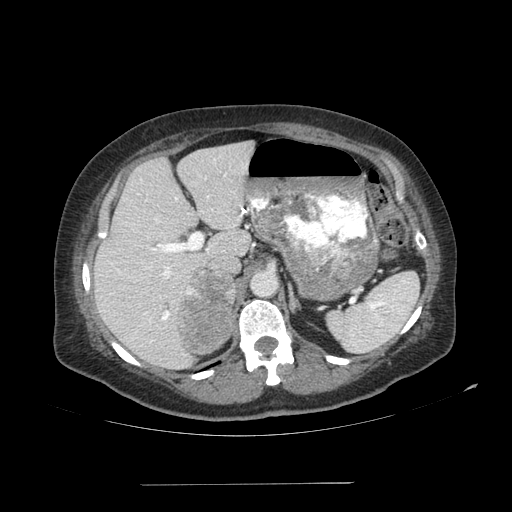
Contrast-enhanced abdominal CT, one axial slice. Slice 69 of 113 in the series (ordered by position). Reconstruction kernel SOFT. 120 kVp. Soft-tissue window (W 400 / L 40 HU). 512 × 512 image matrix, field of view 440 × 440 mm. Patient: female, 67 years. Case-level facts recorded for this patient, not image findings: diagnosis: adrenocortical carcinoma; tumour side: right adrenal; tumour size at pathology: 9.8 cm; Ki-67 index: 59 %; stage (as recorded): 4.
Outlined on this slice (semi-automatic segmentation, software-assisted and operator-edited):
- mass: bounding box (x1, y1, x2, y2) in pixels: (175, 271, 235, 352)